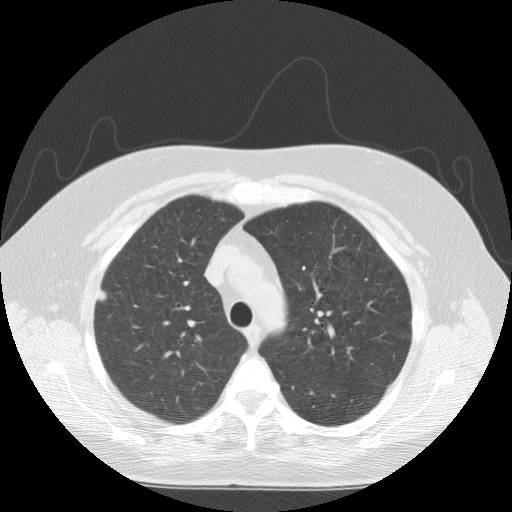
Low-dose screening chest CT, axial slice, baseline screening round, lung window (W 1500 / L -600 HU), 2.5 mm slice thickness, standard (soft-tissue) reconstruction kernel (STANDARD), slice 36 of 146 in the series. Female, age 55 years at enrolment.
Lesion marked by an expert reader, bounding box <86,281,121,318> (left, top, right, bottom; pixels). Screening reader's record for this exam (one nodule recorded; not confirmed to be the boxed lesion): non-calcified nodule or mass ≥4 mm, right upper lobe, 8 × 7 mm, spiculated (stellate) margins, soft tissue attenuation. Official screen result: positive, change unspecified: nodule(s) >= 4 mm or enlarging nodule(s), mass(es), or other non-specific abnormalities suspicious for lung cancer.